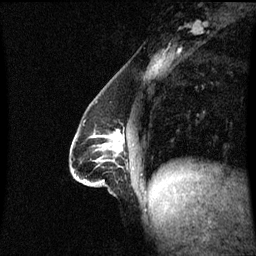
Breast MRI (dynamic contrast-enhanced), one sagittal slice. Position 28 of 60 along the scan axis. Dynamic contrast-enhanced series, image 2 of 3 at this slice position (ordered by acquisition). 1.5 T. TE 4.2 ms, TR 8.9 ms. 2.2 mm slice thickness. 256 × 256 image matrix, field of view 210 × 210 mm. Patient: female, 47 years. Case-level facts recorded for this patient, not image findings: setting: breast cancer imaged before/during neoadjuvant chemotherapy; receptor status: HR-positive, HER2-negative.
Structures marked on this image (semi-automatic segmentation, software-assisted and operator-edited):
- analysis volume of interest (the breast-tissue region the enhancement analysis was run in; not a lesion): bounding box [x1, y1, x2, y2] px = [71, 128, 123, 188]
- tumour enhancement mask (voxels above the 70 % enhancement threshold inside the analysis volume of interest): [116, 133, 122, 151]